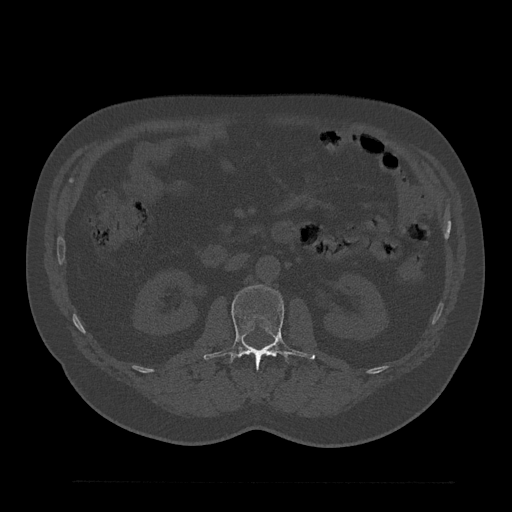
CT including the spine, one axial slice. Position 103 of 797 along the scan axis. Bone window (W 1800 / L 400 HU). 512 × 512 image matrix, field of view 430 × 430 mm. Patient: male, 61 years. Case-level facts recorded for this patient, not image findings: primary cancer: prostate.
Annotated regions visible in this slice (semi-automatically segmented with operator editing):
- L1 vertebra: bounding box (x1, y1, x2, y2) in pixels: (263, 353, 272, 356)
- L2 vertebra: (204, 285, 316, 368)